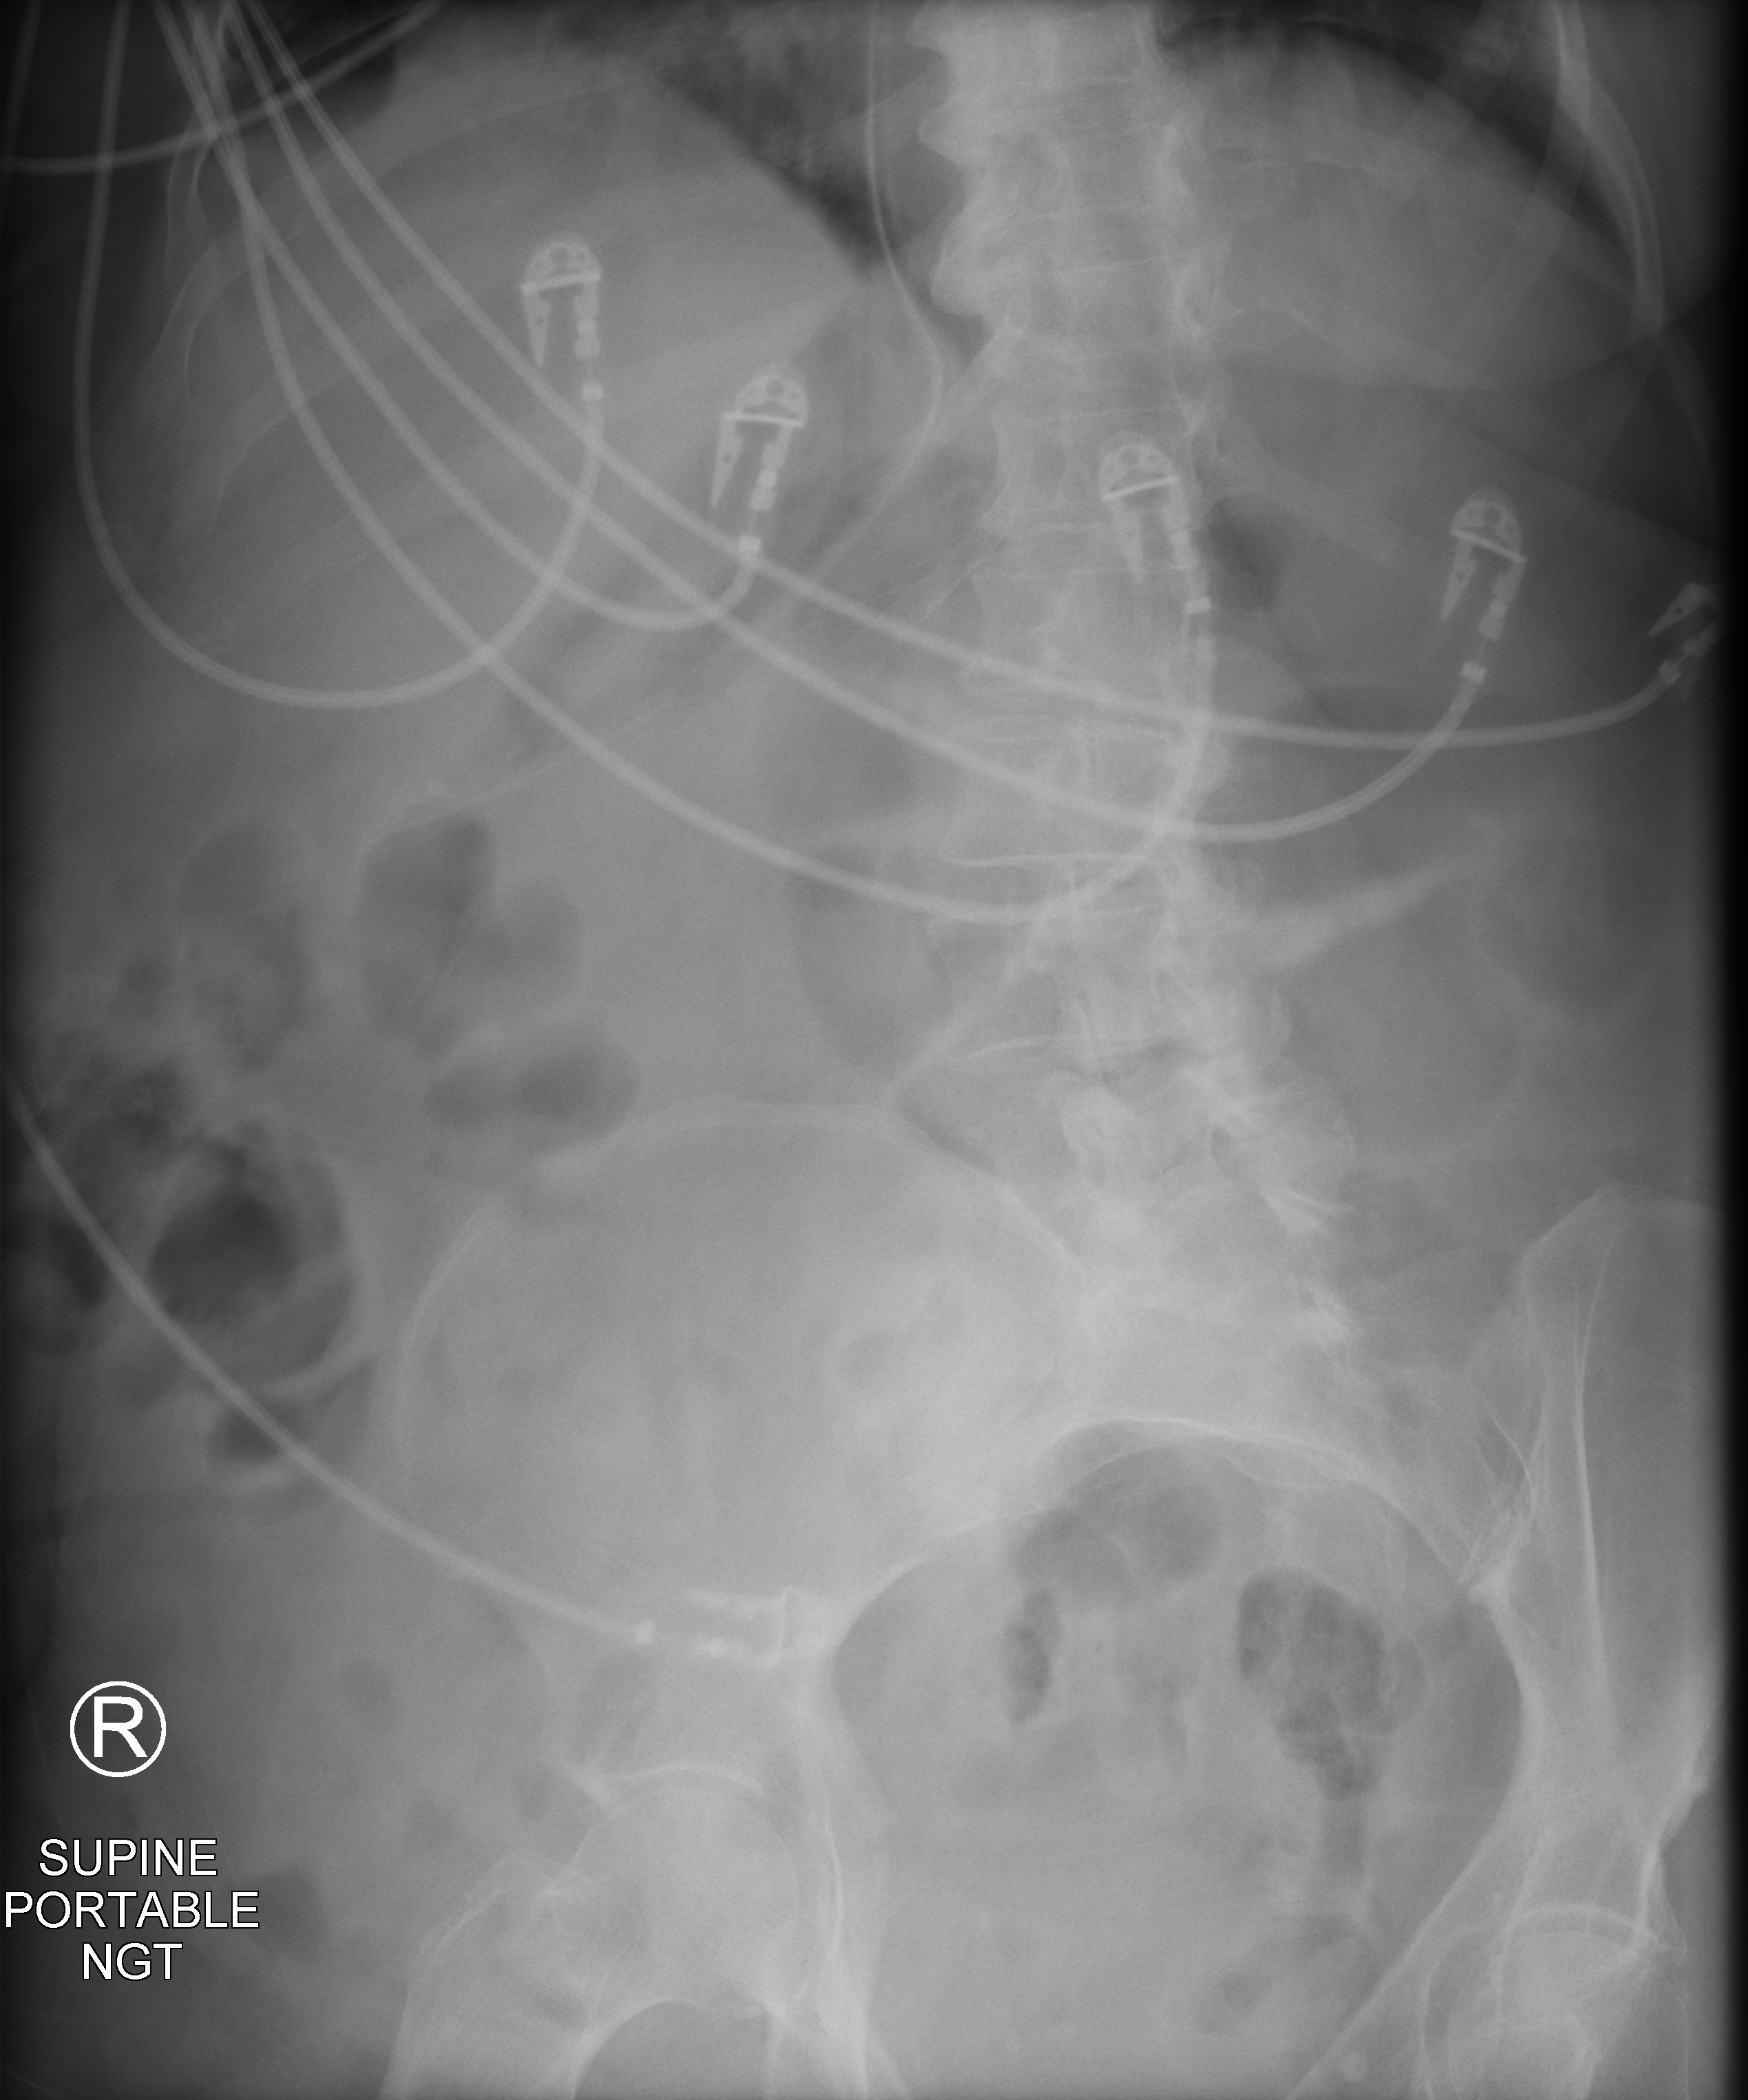
Abdomen X-ray (portable), anteroposterior (AP) projection. Patient hospitalised with COVID-19; female, aged 75–90 years.
From the hospital-stay record, not from the radiograph (when in the stay this image was taken is not recorded):
- diabetes (admission record): no
- mechanically ventilated during this hospital stay: yes
- admitted to intensive care during this hospital stay: yes